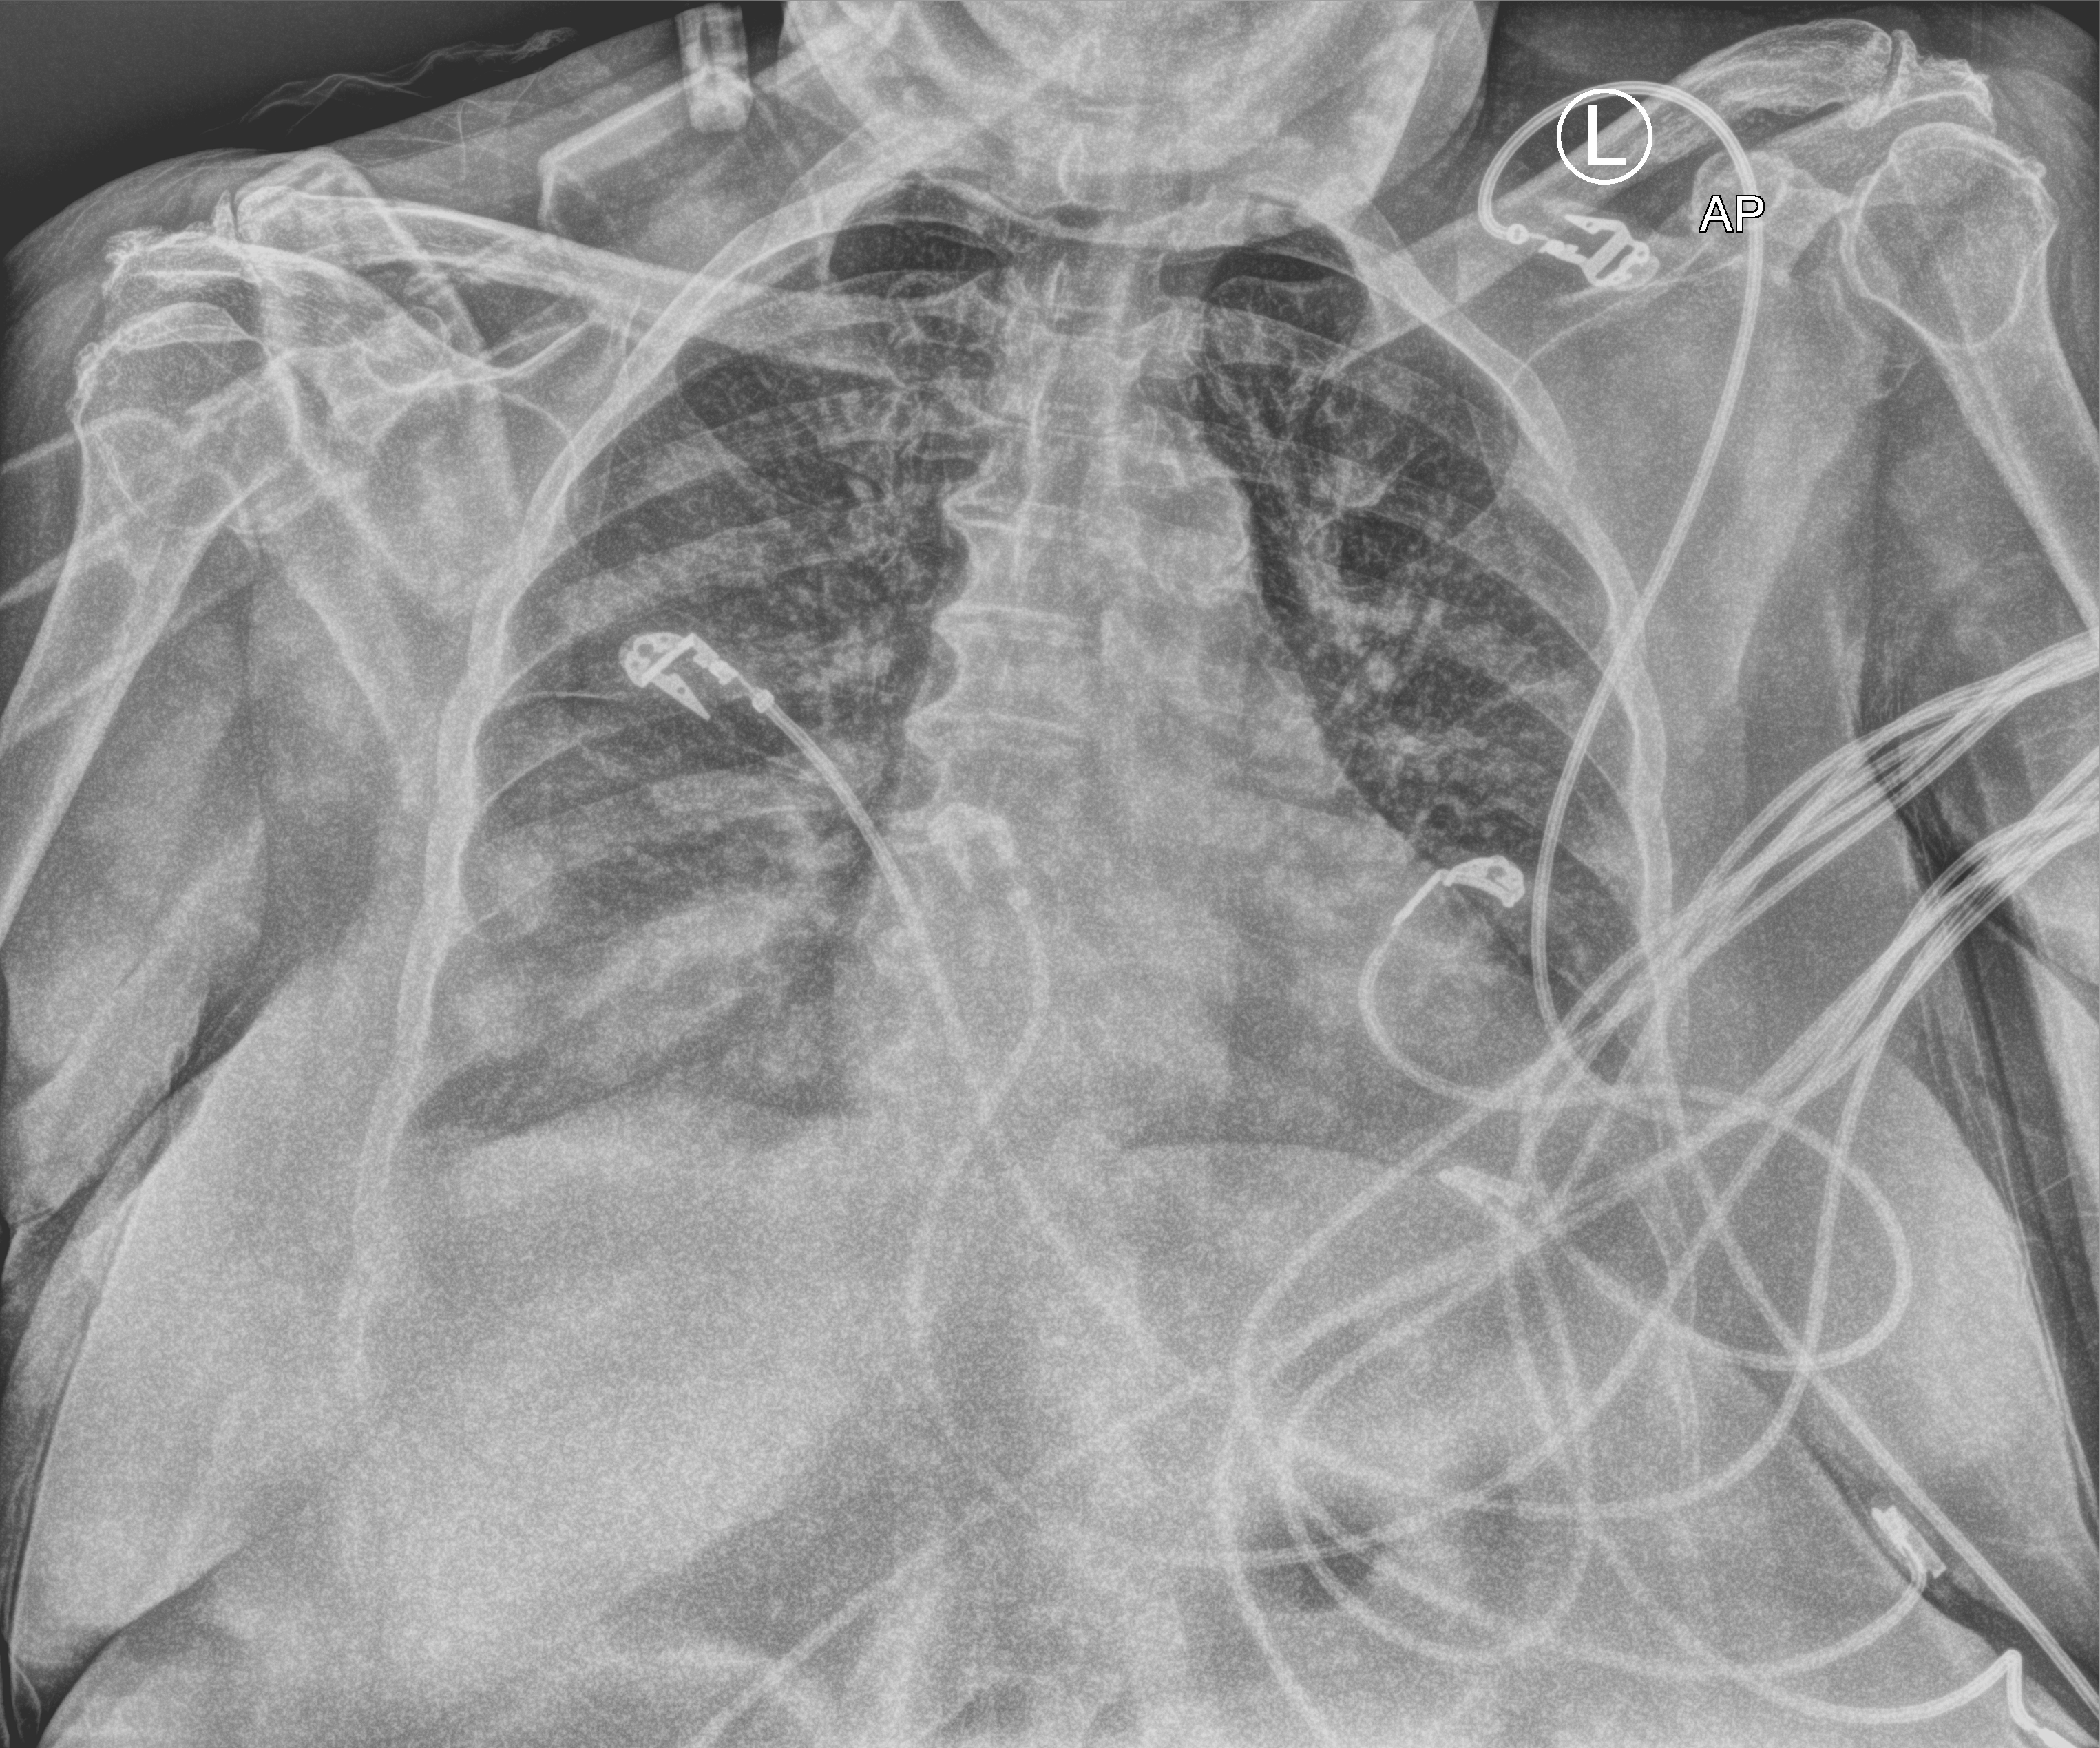
Bedside chest radiograph (computed radiography), anteroposterior (AP) projection. Female patient hospitalised with COVID-19, age 75–90 years.
From the hospital-stay record, not from the radiograph (when in the stay this image was taken is not recorded):
- admitted to intensive care during this hospital stay: no
- length of hospital stay: 4 days
- mechanically ventilated during this hospital stay: no